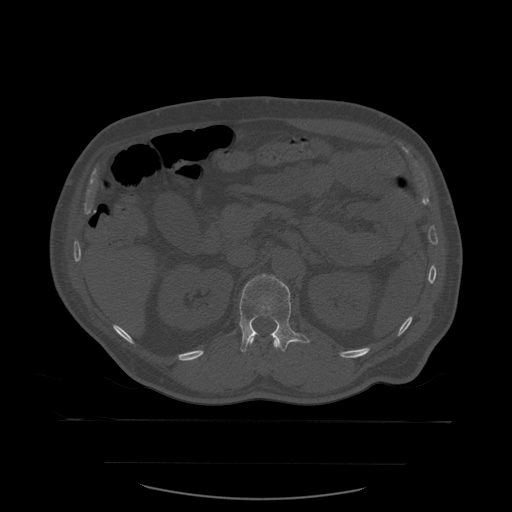
CT including the spine, one axial slice; slice 251 of 590 in the series (ordered by position); bone window (W 1800 / L 400 HU); 1.25 mm slice thickness; 512 × 512 image matrix, field of view 479 × 479 mm. Patient age 71 years. Case-level facts recorded for this patient, not image findings: primary cancer: lung; vertebrae with lytic lesions (as recorded): T1, T2, L5, S1.
Structures marked on this image (semi-automatic segmentation, software-assisted and operator-edited):
- L1 vertebra: box from (x=239, y=274) to (x=311, y=353) px
- T12 vertebra: (x=251, y=339)–(x=287, y=352)